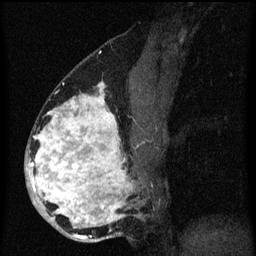
Breast MRI (dynamic contrast-enhanced), one sagittal slice; slice 33 of 60 in the series (ordered by position); dynamic contrast-enhanced series, image 2 of 3 at this slice position (ordered by acquisition); 1.5 T; TE 4.2 ms, TR 8.4 ms; 2 mm slice thickness; 256 × 256 image matrix, field of view 180 × 180 mm. Patient: female, 34 years. Case-level facts recorded for this patient, not image findings: setting: breast cancer imaged before/during neoadjuvant chemotherapy; receptor status: HR-positive, HER2-negative.
Outlined on this slice (semi-automatic segmentation, software-assisted and operator-edited):
- analysis volume of interest (the breast-tissue region the enhancement analysis was run in; not a lesion): bounding box <26,58,155,243> (left, top, right, bottom; pixels)
- tumour enhancement mask (voxels above the 70 % enhancement threshold inside the analysis volume of interest): <26,82,133,239>